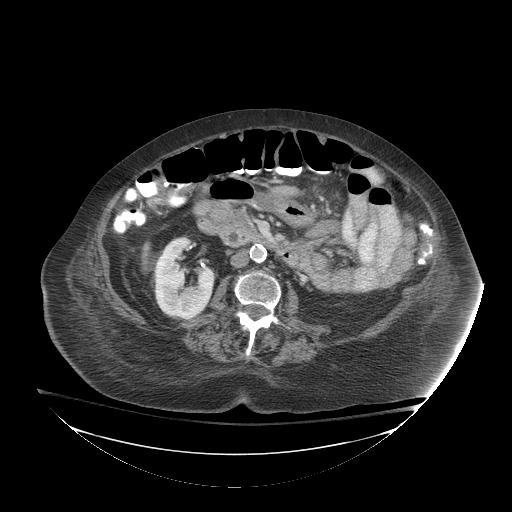
Contrast-enhanced abdominal CT (liver protocol), one axial slice; slice 20 of 81 in the series (ordered by position); reconstruction kernel STANDARD; 140 kVp; soft-tissue window (W 400 / L 40 HU); 2.5 mm slice thickness; 512 × 512 image matrix, field of view 500 × 500 mm. From the clinical record (not read from this slice): diagnosis: hepatocellular carcinoma (patient treated with transarterial chemoembolisation; whether this scan precedes or follows treatment is not stated here); TNM stage (as recorded): Stage-I; Child-Pugh class: B; tumour differentiation: well-moderately differentiated.
Structures marked on this image (semi-automatic segmentation, software-assisted and operator-edited):
- liver parenchyma outside the tumour (the mass and vessels are separate outlines, so this box may not span the whole liver): bounding box <140,244,148,268> (left, top, right, bottom; pixels)